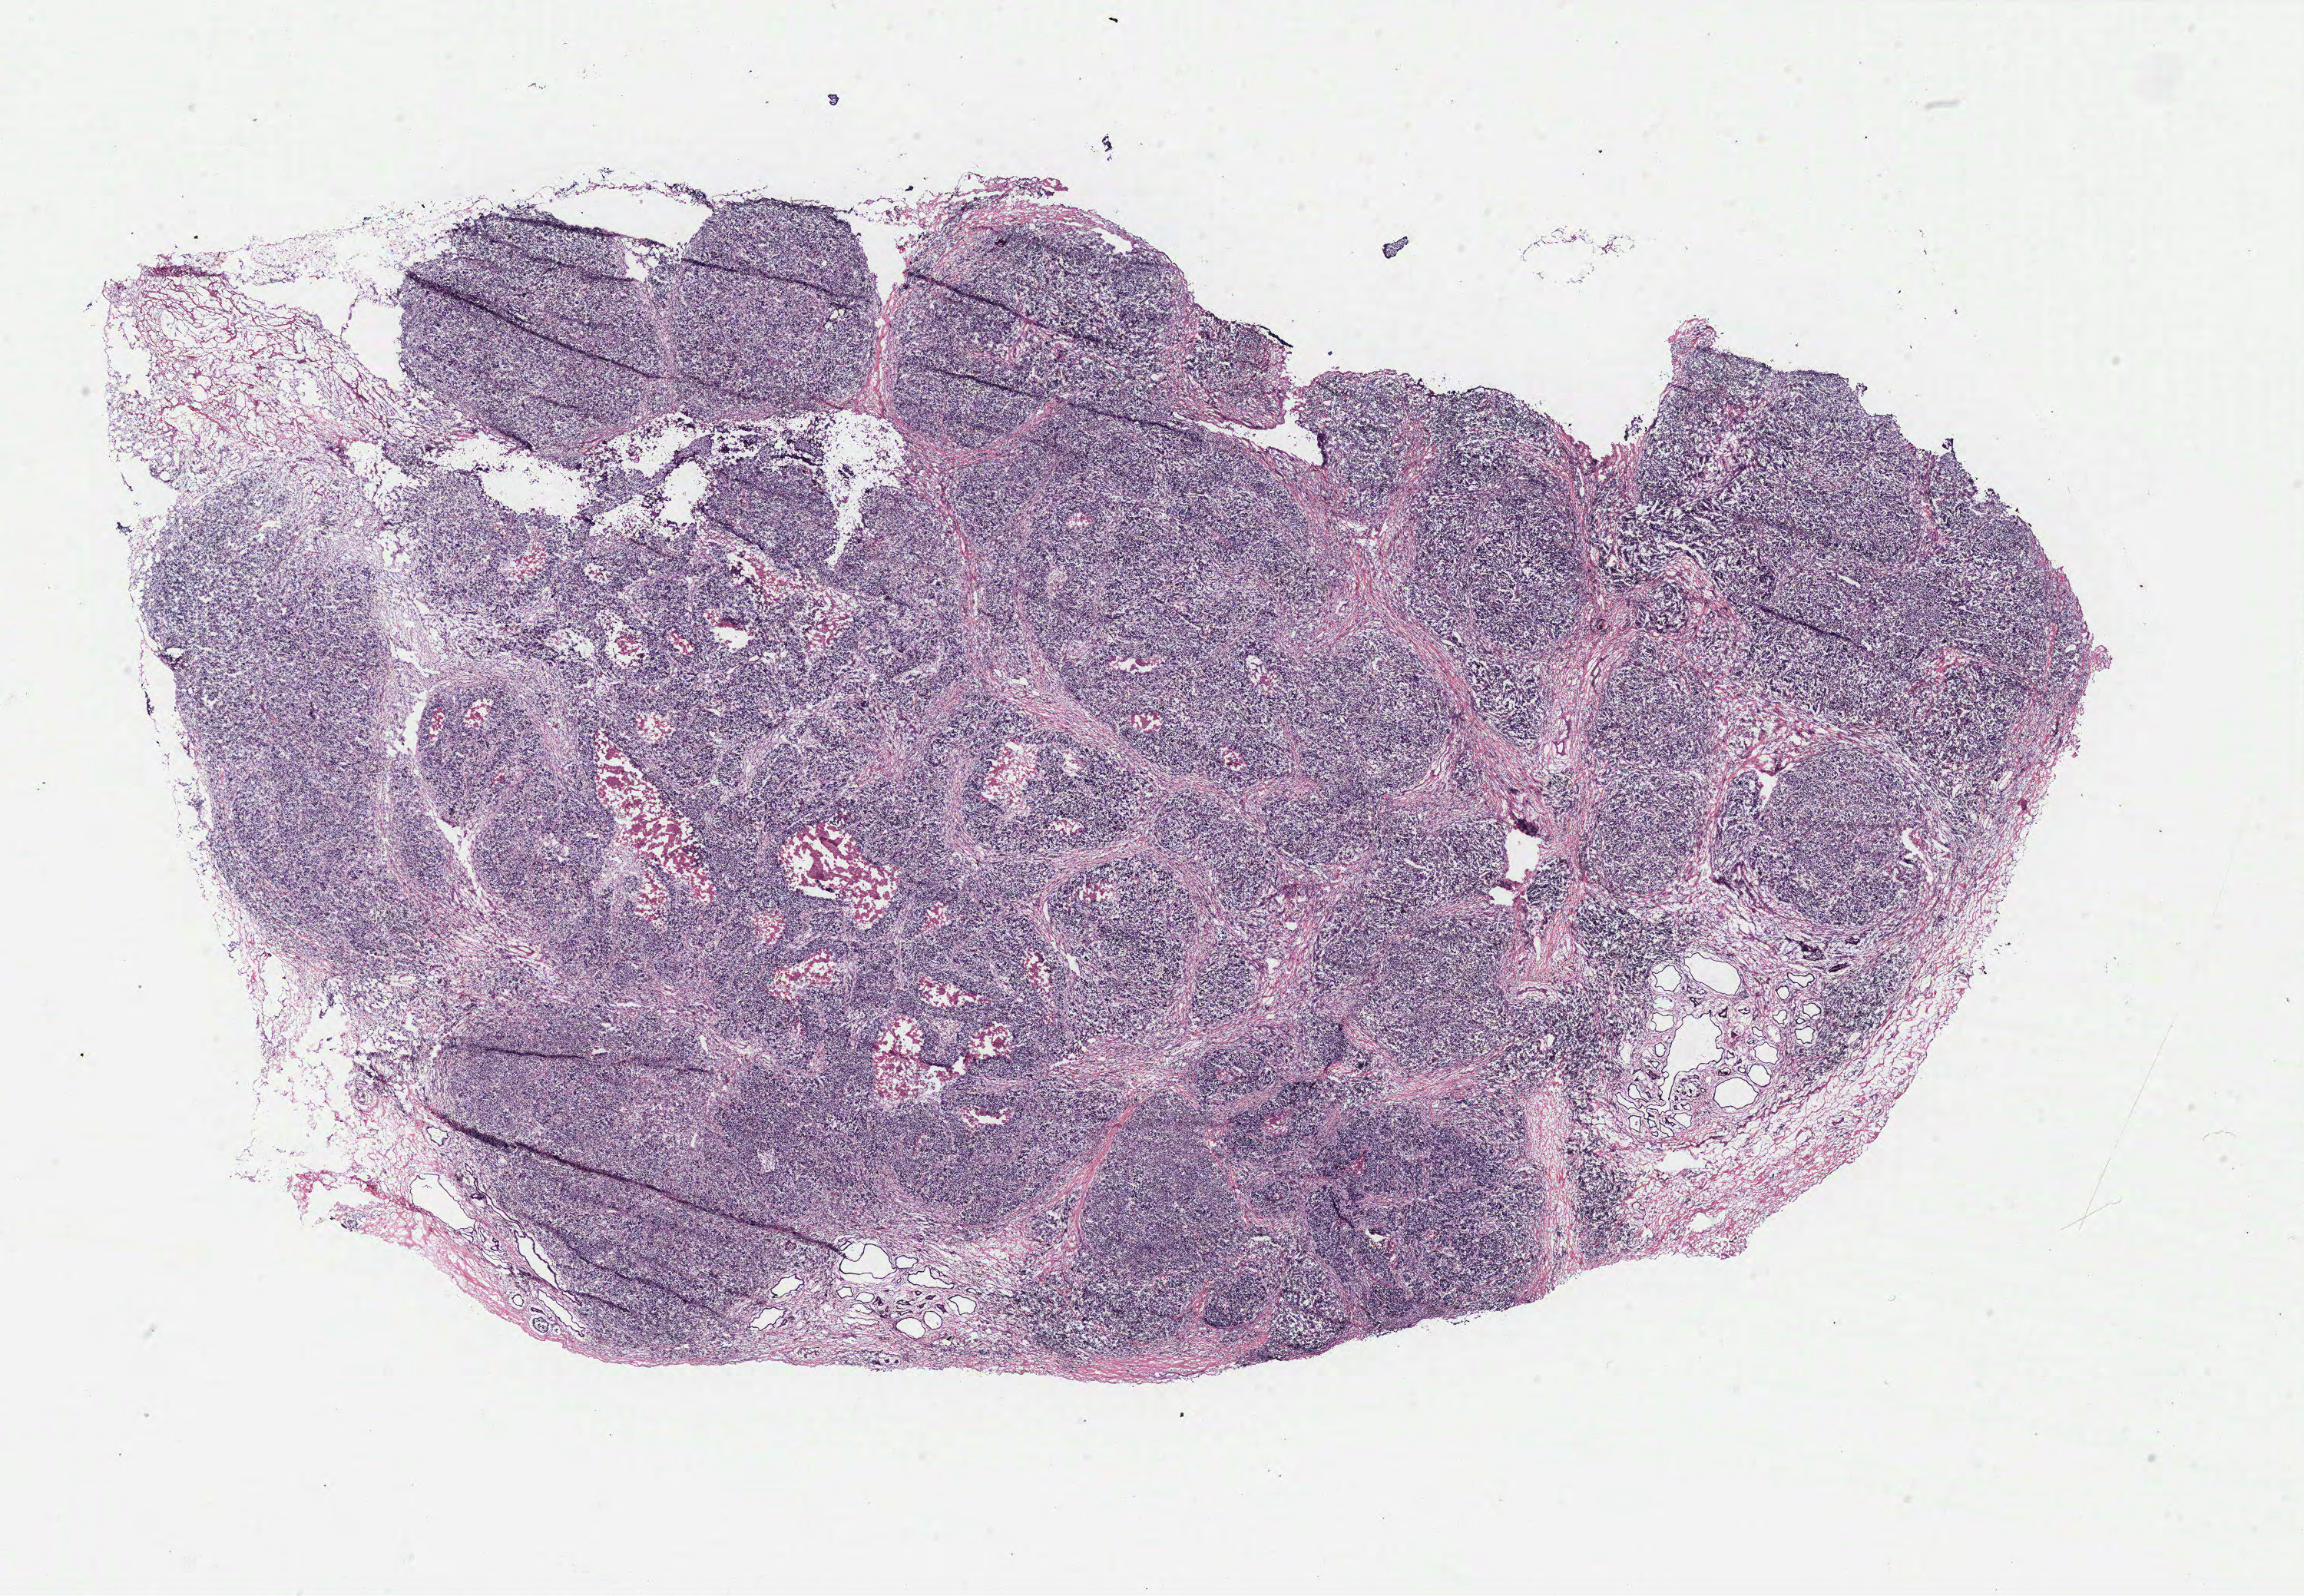
Hematoxylin and eosin (H&E) stained whole-slide image — a low-resolution overview of the entire scanned area, about 24.0 x 16.6 mm. Breast, tissue type not recorded. Patient: female, age 53 years.
• patient diagnosis: Infiltrating duct carcinoma, NOS